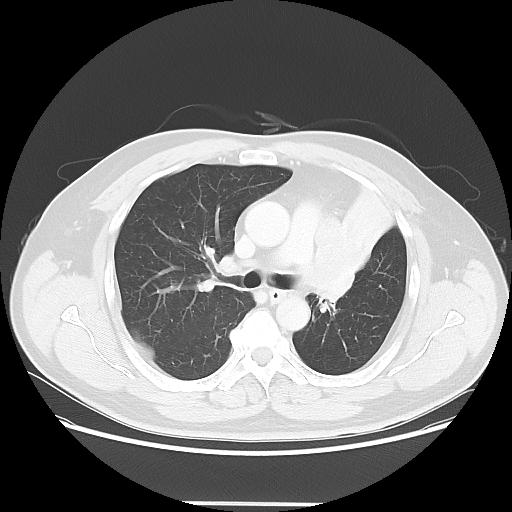
Chest CT, one axial slice; slice 39 of 62 in the series (ordered by position); lung window (W 1500 / L -600 HU); 512 × 512 image matrix. Male patient, age 49 years. From the clinical record (not read from this slice): clinical TNM (as recorded): T3 N3 M1c.
Annotated regions visible in this slice (bounding box drawn by a radiologist):
- lung tumour (recorded histology: squamous cell carcinoma): bounding box (x1, y1, x2, y2) in pixels: (307, 219, 384, 312)